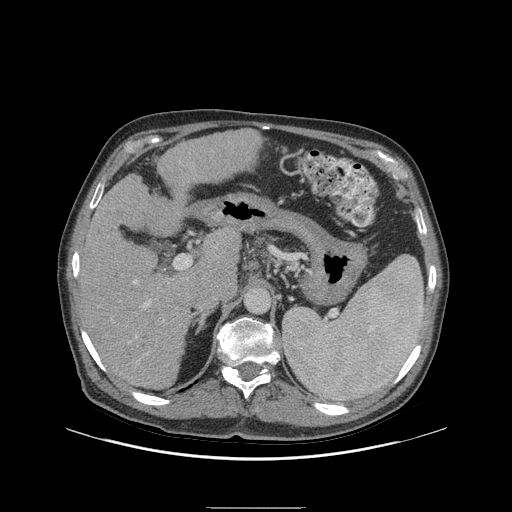
Contrast-enhanced abdominal CT (liver protocol), one axial slice. Position 57 of 105 along the scan axis. 140 kVp. Soft-tissue window (W 400 / L 40 HU). 2.5 mm slice thickness. 512 × 512 image matrix, field of view 440 × 440 mm. Case-level facts recorded for this patient, not image findings: diagnosis: hepatocellular carcinoma (patient treated with transarterial chemoembolisation; whether this scan precedes or follows treatment is not stated here); TNM stage (as recorded): Stage-I; Child-Pugh class: A.
Annotated regions visible in this slice (semi-automatically segmented with operator editing):
- liver parenchyma outside the tumour (the mass and vessels are separate outlines, so this box may not span the whole liver): bounding box <76,136,238,388> (left, top, right, bottom; pixels)
- liver vessels: <134,280,151,337>